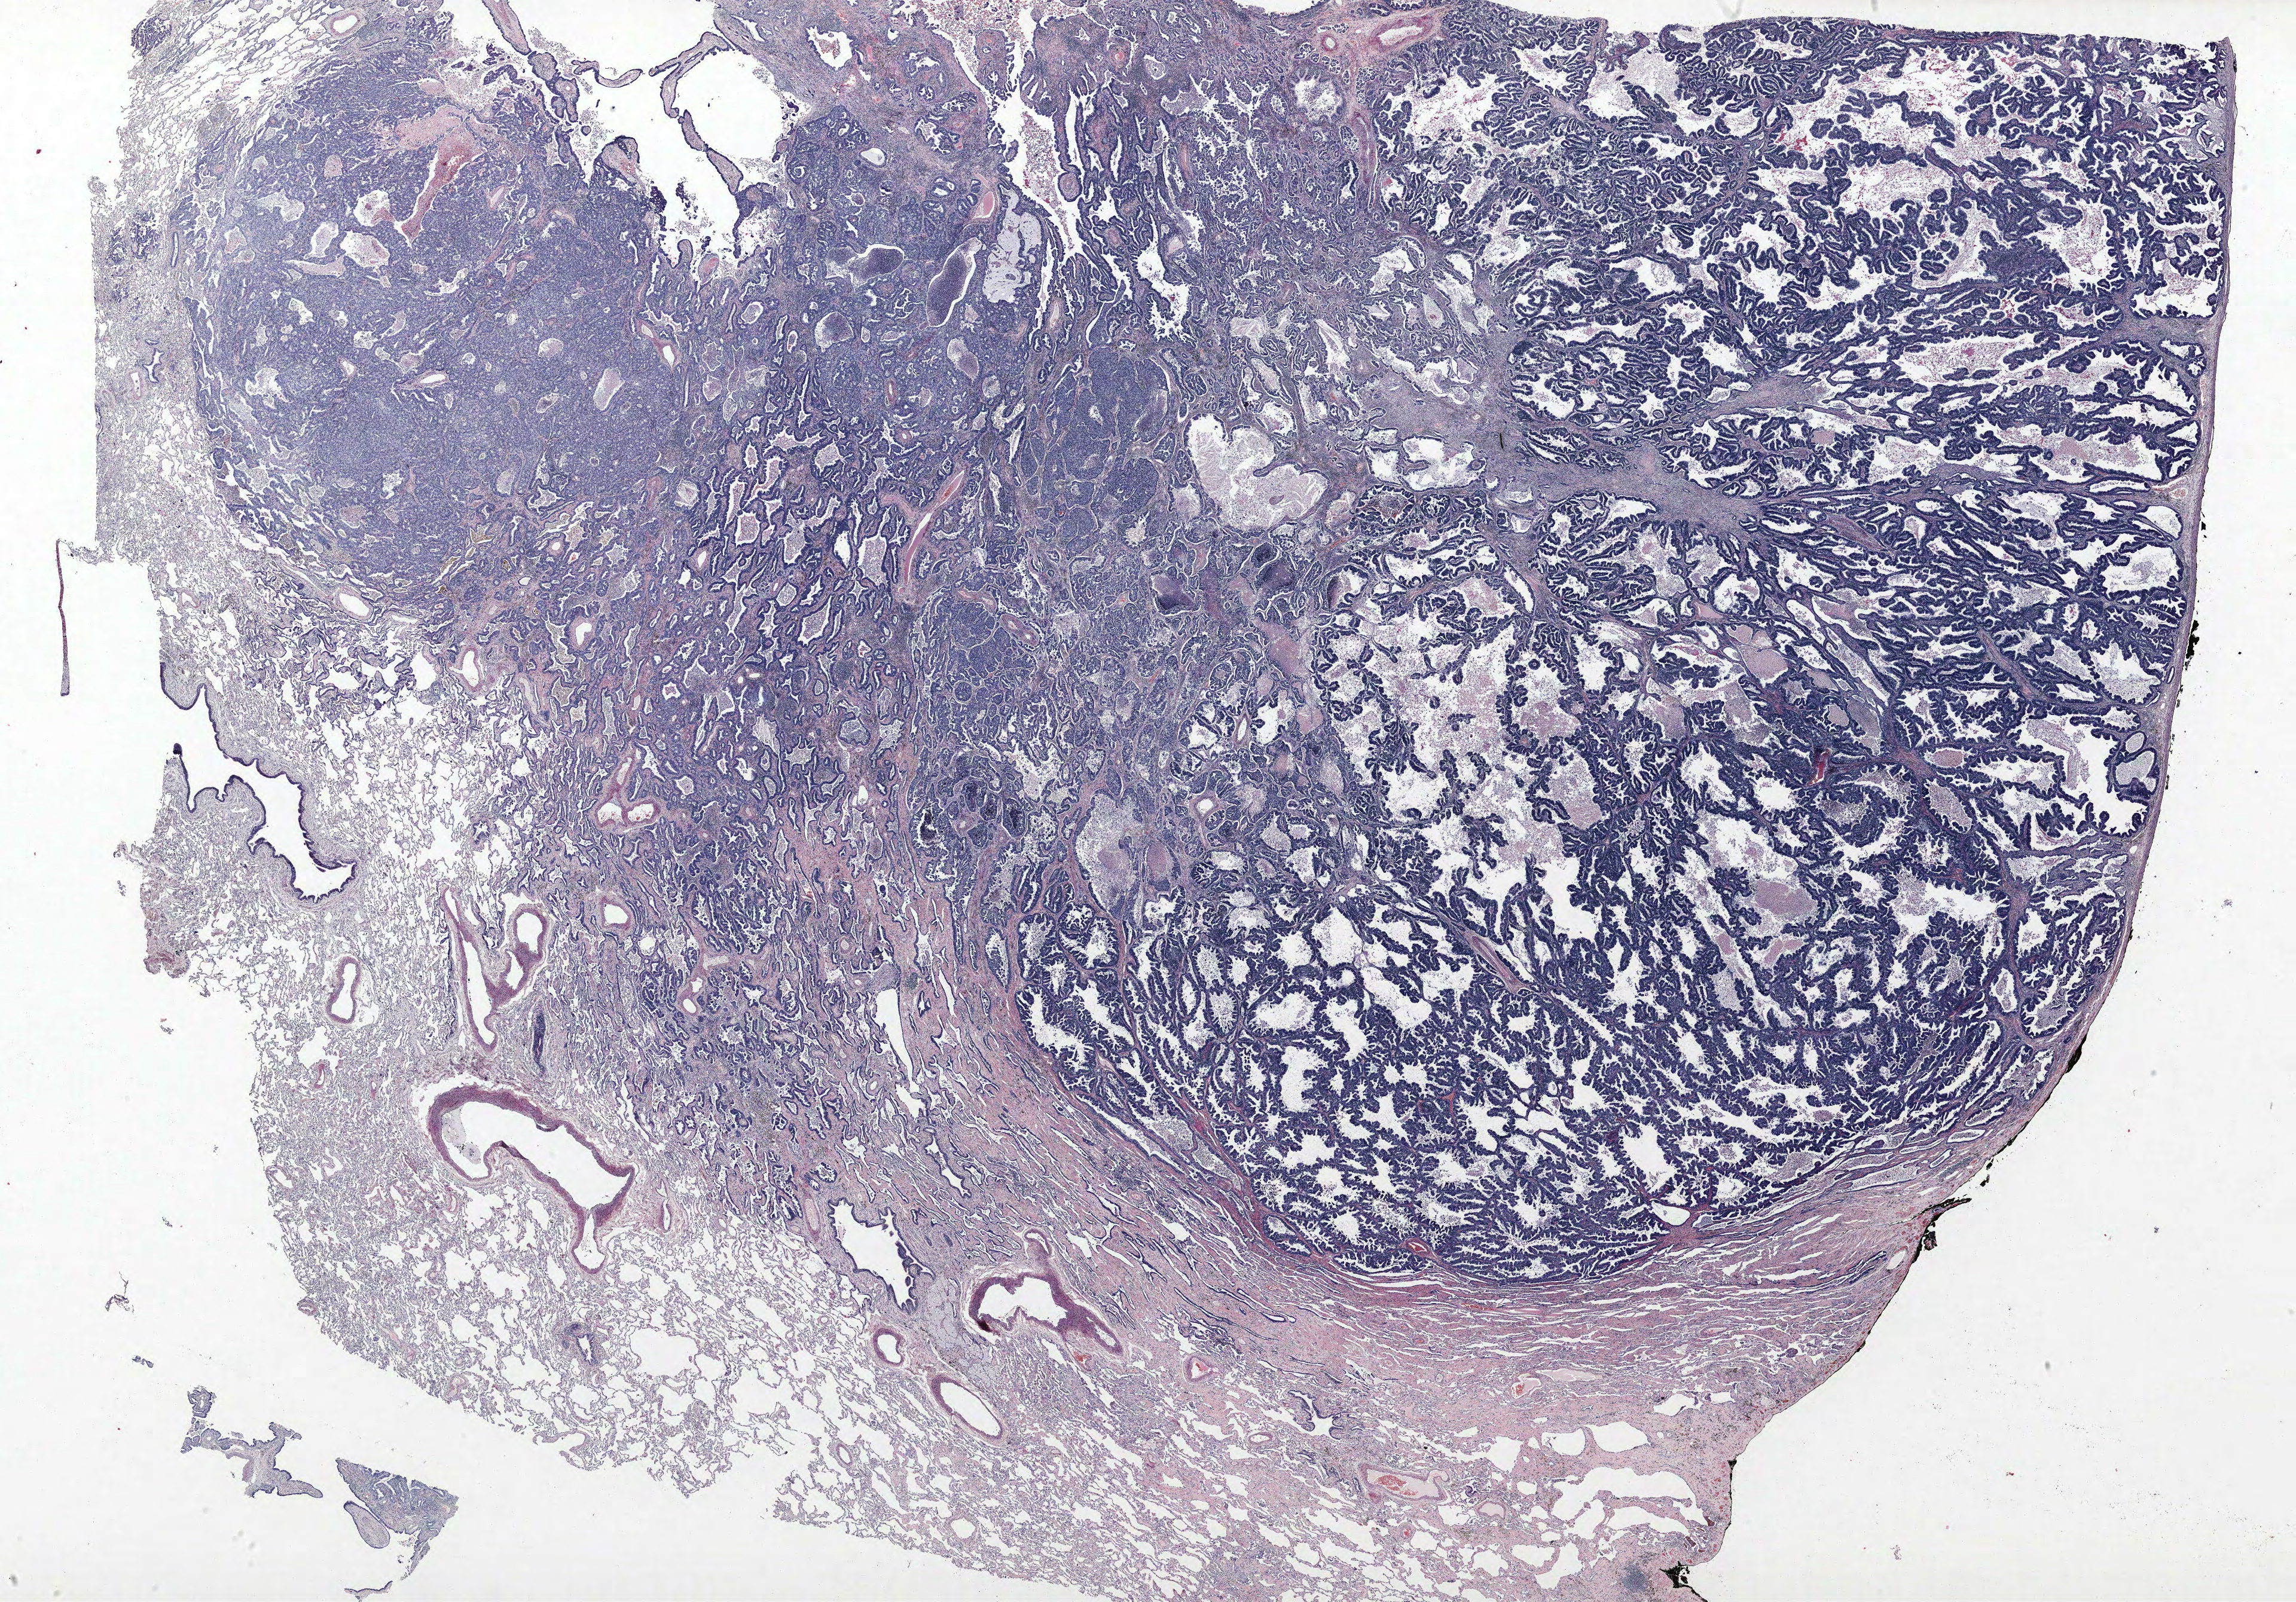
Hematoxylin and eosin (H&E) stained whole-slide image, low-resolution overview of the scanned area, about 30.7 x 21.4 mm (from a 40x scan), FFPE section, lung. Male patient, aged 55 at enrolment. Current smoker at enrolment. Grade: moderately differentiated (G2).
Participant's lung-cancer diagnosis: Adenocarcinoma, NOS. ICD-O-3 topography: lower lobe of lung (C34.3). Tumour size (pathology): 75 mm. Stage (AJCC 6th edition): IB. Primary tumour location (clinical record): right lower lobe. Note: participant had 2 primary lung cancers recorded; fields above describe the first.